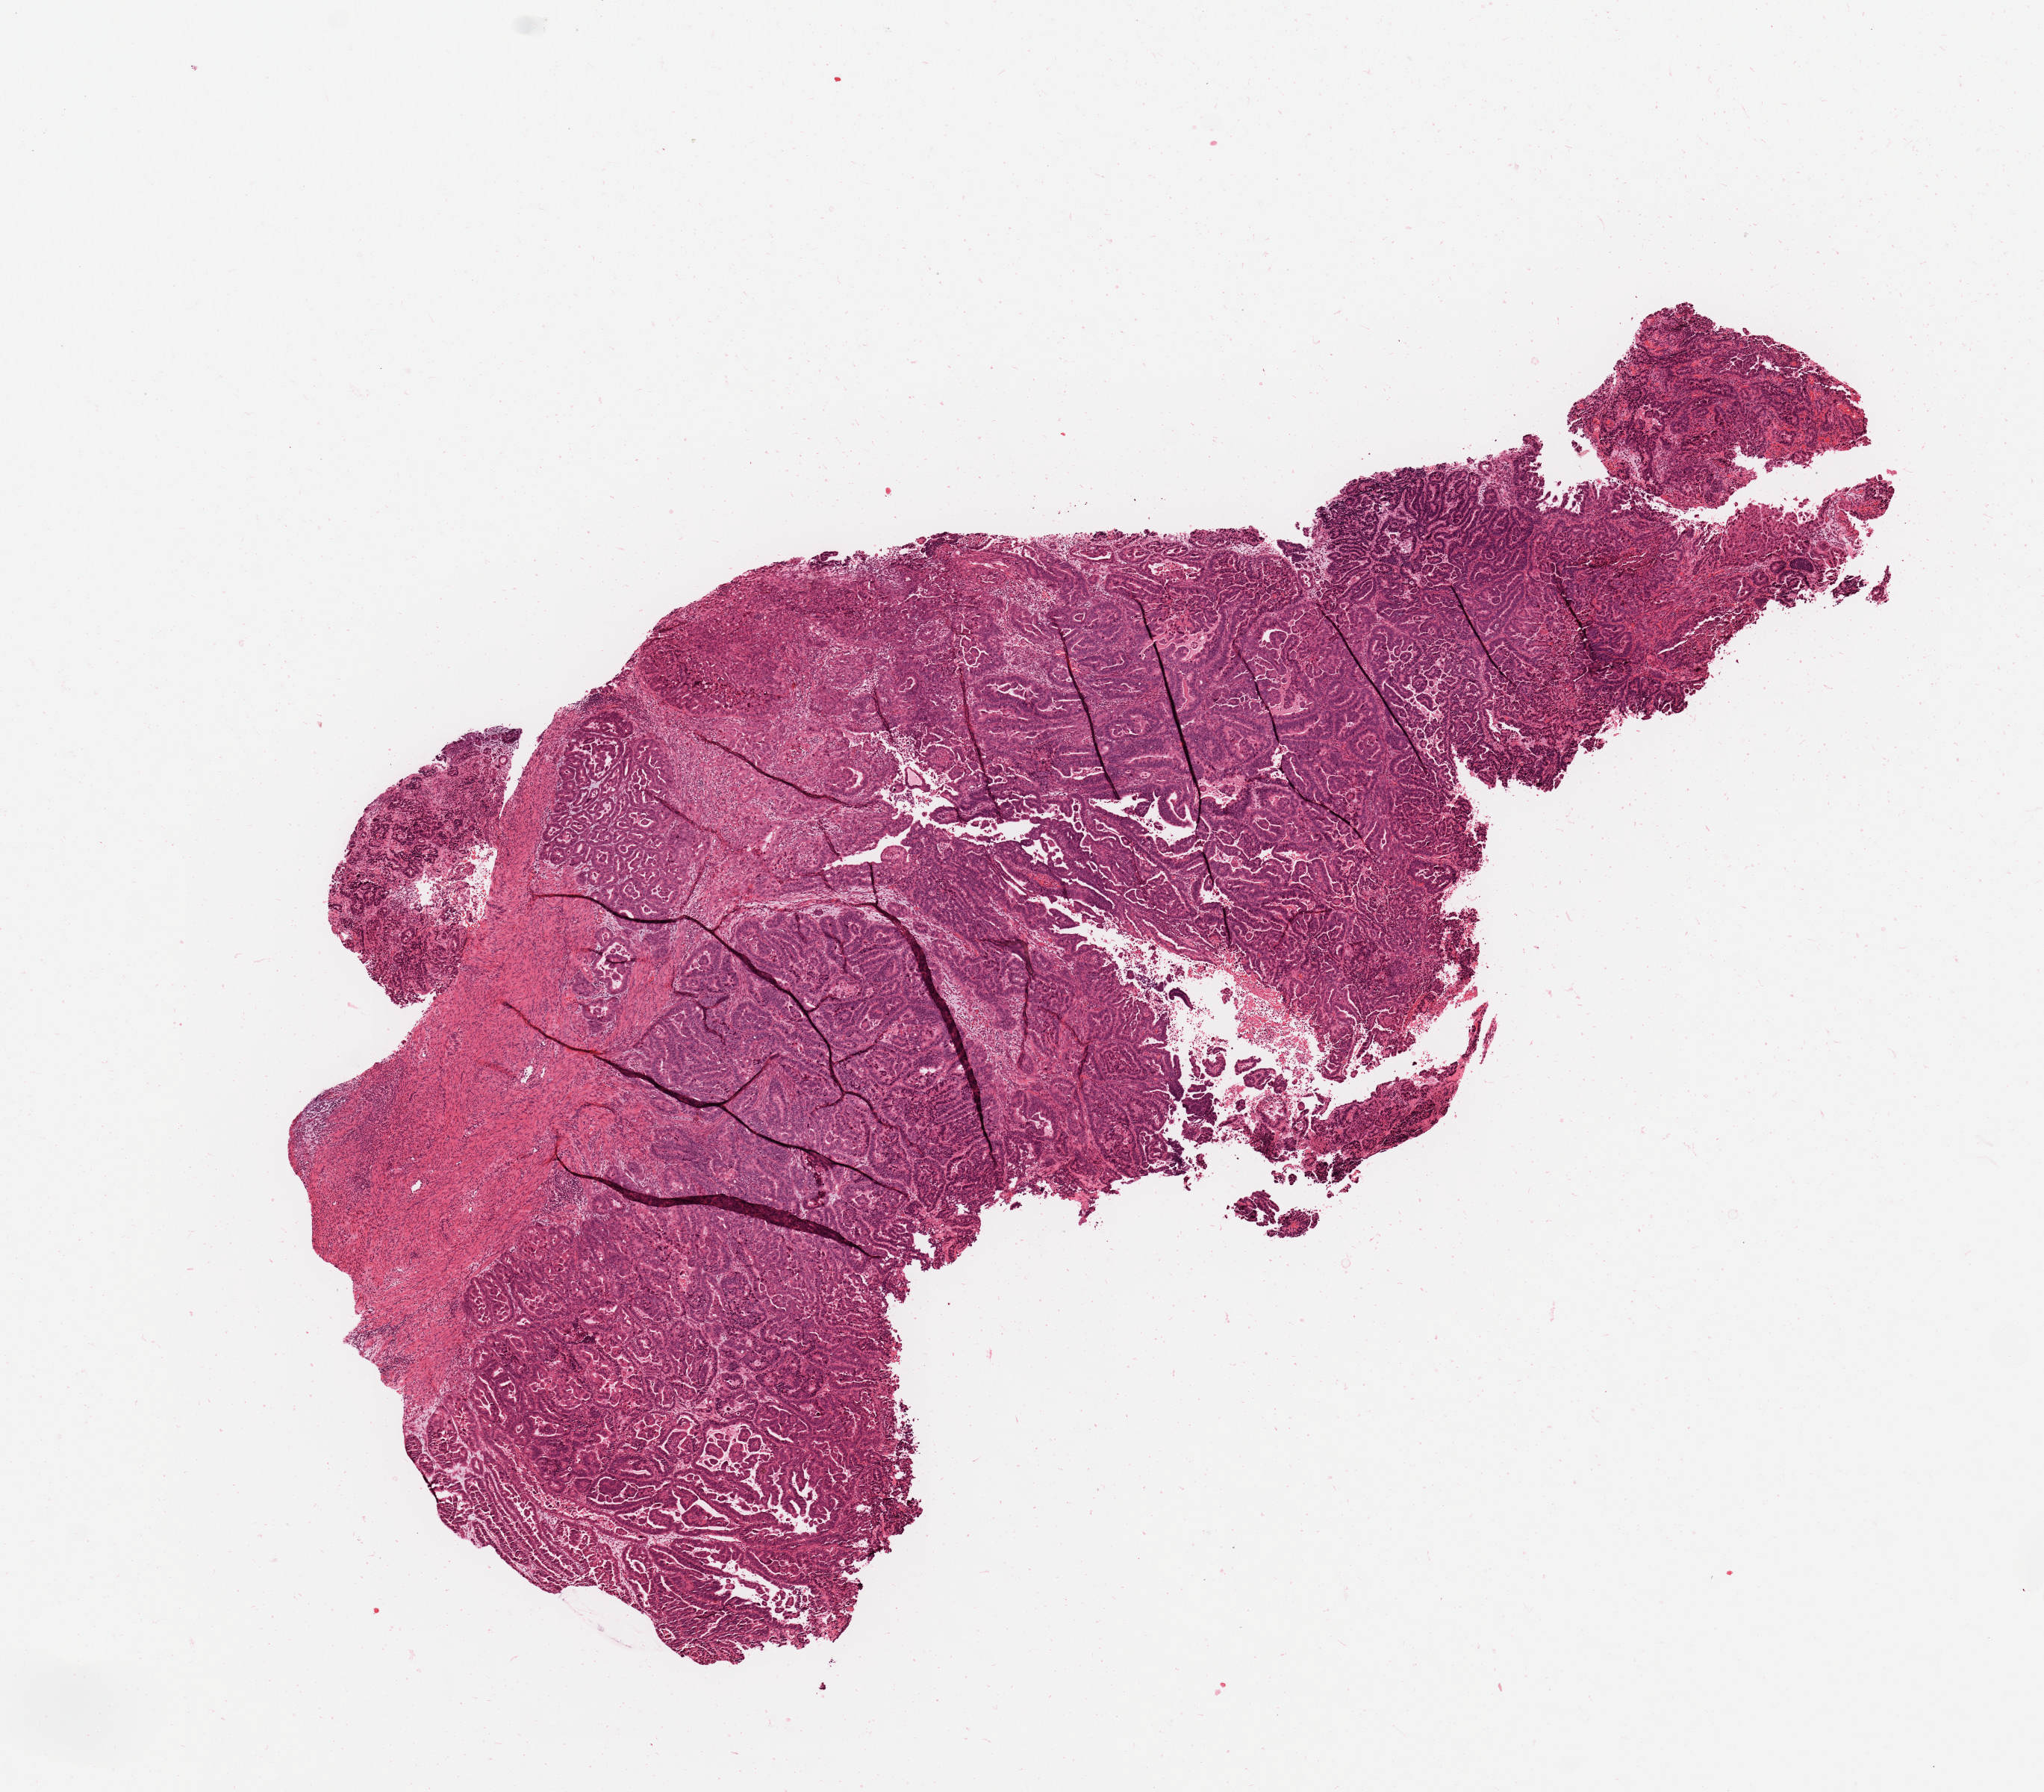
Digitized H&E-stained tissue section (whole slide), shown as a low-resolution overview of the whole scanned area (about 10.8 x 9.5 mm, acquisition: 20x scan). Tumour tissue sample, sampled site: uterus. 73-year-old female patient. Histologic grade: G3 (poorly differentiated). Composition of this section per pathologist review: tumour nuclei 80%, necrosis 0%.
Diagnosis: Endometrioid adenocarcinoma, NOS. AJCC pathologic stage: IIIC1.